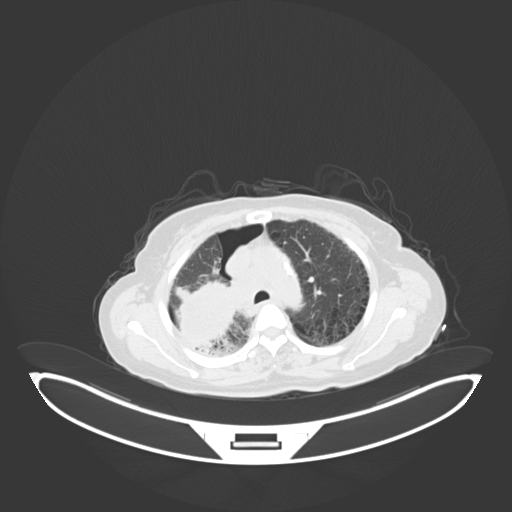
Chest CT, one axial slice; position 44 of 69 along the scan axis; reconstruction kernel B30f; 120 kVp; lung window (W 1500 / L -600 HU); 3 mm slice thickness; 512 × 512 image matrix, field of view 500 × 500 mm. Patient: female, 64 years. From the clinical record (not read from this slice): clinical TNM (as recorded): T3 N3 M0.
Structures marked on this image (rectangle marked by the reading radiologist):
- lung tumour (recorded histology: squamous cell carcinoma): box from (x=166, y=278) to (x=239, y=349) px